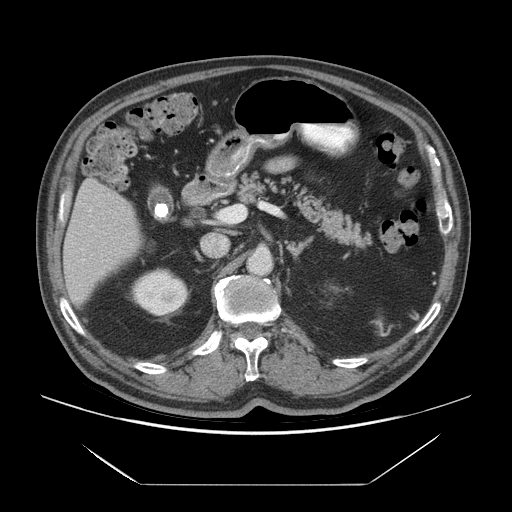
Contrast-enhanced abdominal CT (liver protocol), one axial slice; position 31 of 75 along the scan axis; reconstruction kernel STANDARD; 140 kVp; soft-tissue window (W 400 / L 40 HU); 2.5 mm slice thickness; 512 × 512 image matrix, field of view 420 × 420 mm. From the clinical record (not read from this slice): diagnosis: hepatocellular carcinoma (patient treated with transarterial chemoembolisation; whether this scan precedes or follows treatment is not stated here); TNM stage (as recorded): Stage-I; Child-Pugh class: A; tumour differentiation: well differentiated; tumour nodularity: uninodular.
Outlined on this slice (semi-automatic segmentation, software-assisted and operator-edited):
- liver parenchyma outside the tumour (the mass and vessels are separate outlines, so this box may not span the whole liver): bounding box <62,178,140,306> (left, top, right, bottom; pixels)